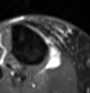
MRI of an extremity soft-tissue mass, one axial slice. Position 40 of 60 along the scan axis. STIR. MR volume resampled by the dataset authors to the PET/CT grid (not the native acquisition matrix). 90 × 93 image matrix, field of view 88 × 91 mm. Female patient. From the clinical record (not read from this slice): histological type: undifferentiated – high grade; grade: high; site of the primary tumour: right thigh.
Outlined on this slice (expert contour drawn on MRI and transferred to this co-registered scan by the dataset authors):
- gross tumour volume (mass): box from (x=46, y=49) to (x=61, y=70) px